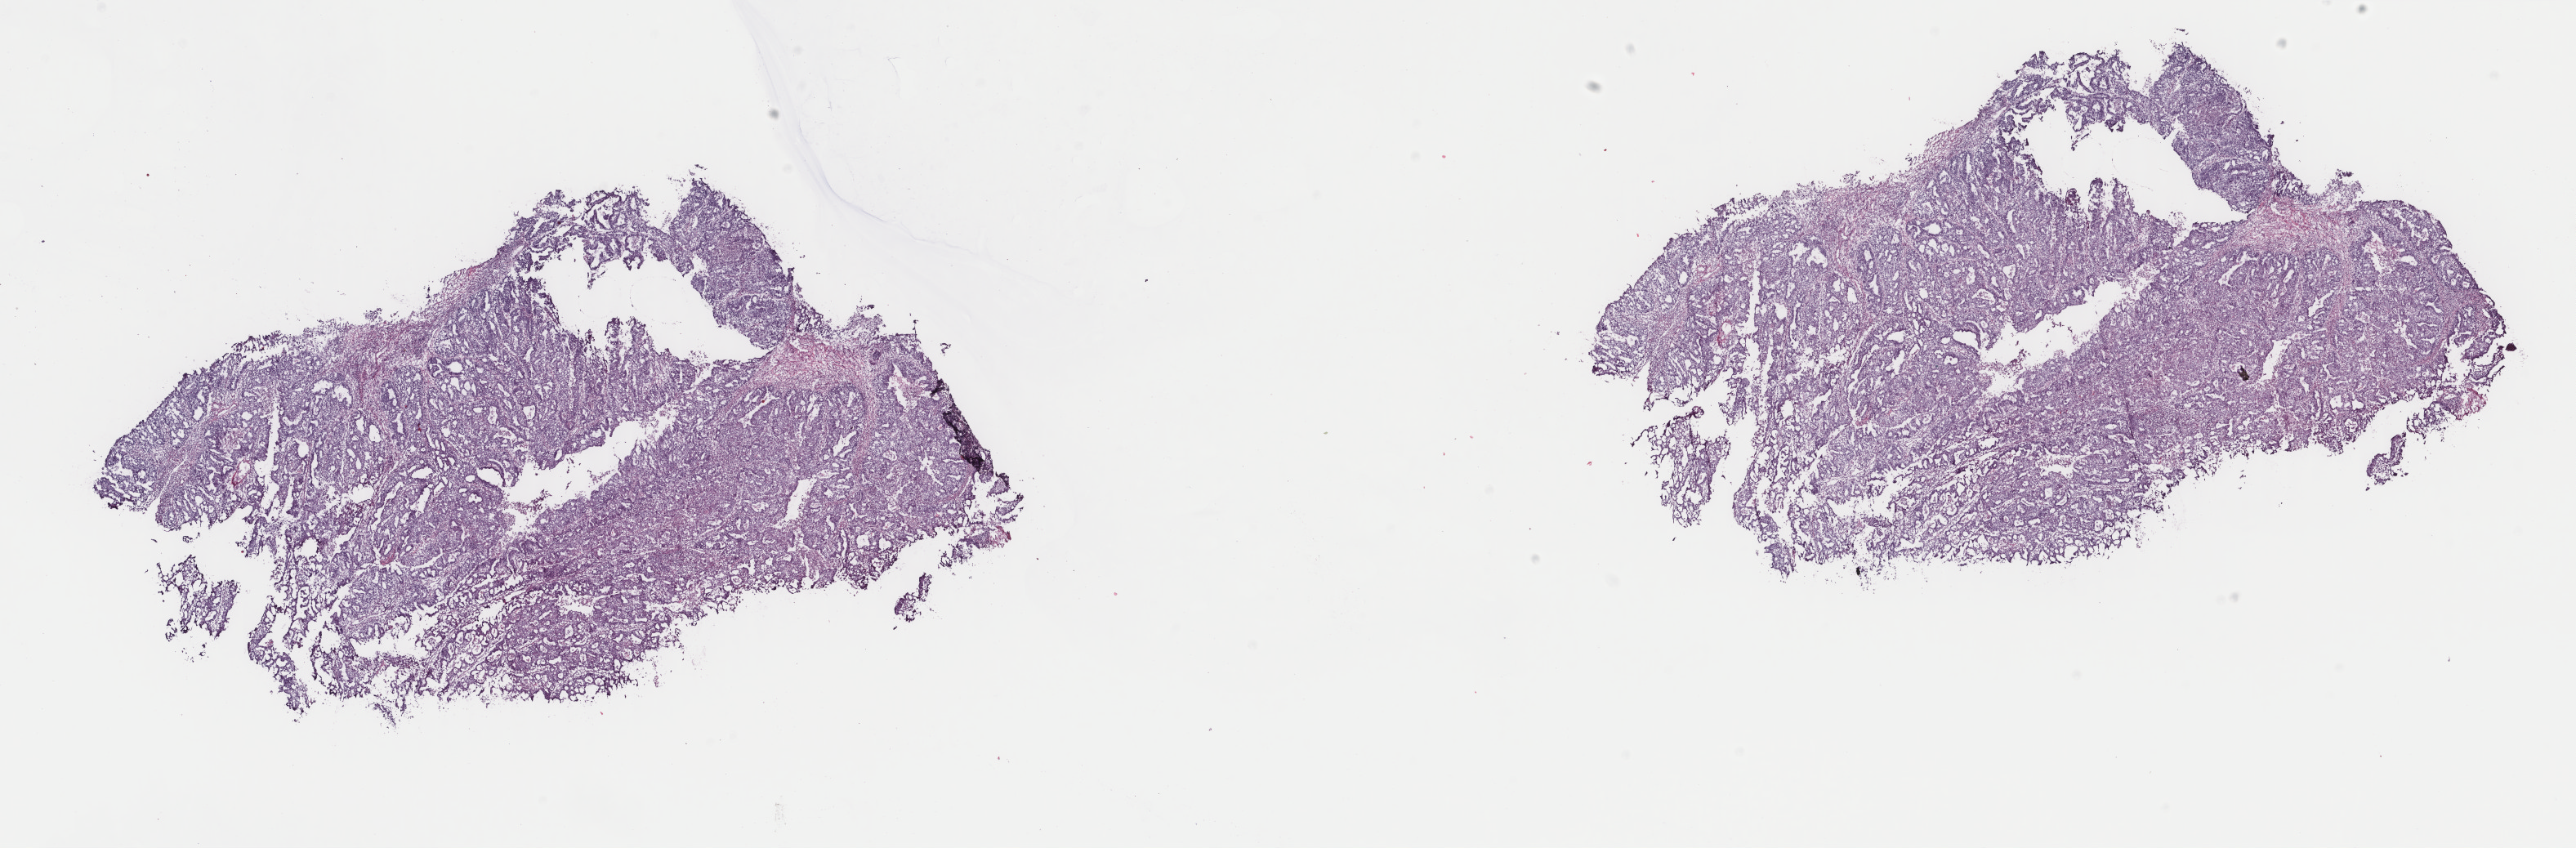
Digitized Hematoxylin and eosin (H&E) stained tissue section (whole slide), a low-resolution overview of the entire scanned area, about 25.0 x 8.2 mm (acquisition: 40x scan), frozen section, primary tumour sample from the uterus. Female, age 76 years at initial diagnosis. Histologic grade: G3 (poorly differentiated). Slide review estimates, as recorded: tumour cells 100%, tumour nuclei 95%, normal cells 0%, stromal cells 0%, necrosis 0%. Inflammatory infiltration, as recorded: lymphocyte infiltration 1%, monocyte infiltration 0%, neutrophil infiltration 0%.
FIGO stage: IA. Diagnosis: Endometrioid adenocarcinoma, NOS (endometrium).